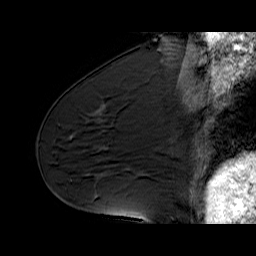
Breast MRI (dynamic contrast-enhanced), one sagittal slice. Position 29 of 60 along the scan axis. Dynamic contrast-enhanced series, time point 2 of 6 at this slice position (early post-contrast). 1.5 T. TE 6.3 ms, TR 32.9 ms. 4 mm slice thickness. 256 × 256 image matrix, field of view 200 × 200 mm. Female patient. Case-level facts recorded for this patient, not image findings: setting: breast cancer imaged before/during neoadjuvant chemotherapy; receptor status: HER2-positive.
Structures marked on this image (semi-automatically segmented with operator editing):
- analysis volume of interest (the breast-tissue region the enhancement analysis was run in; not a lesion): box from (x=48, y=112) to (x=164, y=194) px
- tumour enhancement mask (voxels above the 100 % enhancement threshold inside the analysis volume of interest): (x=70, y=136)–(x=73, y=138)